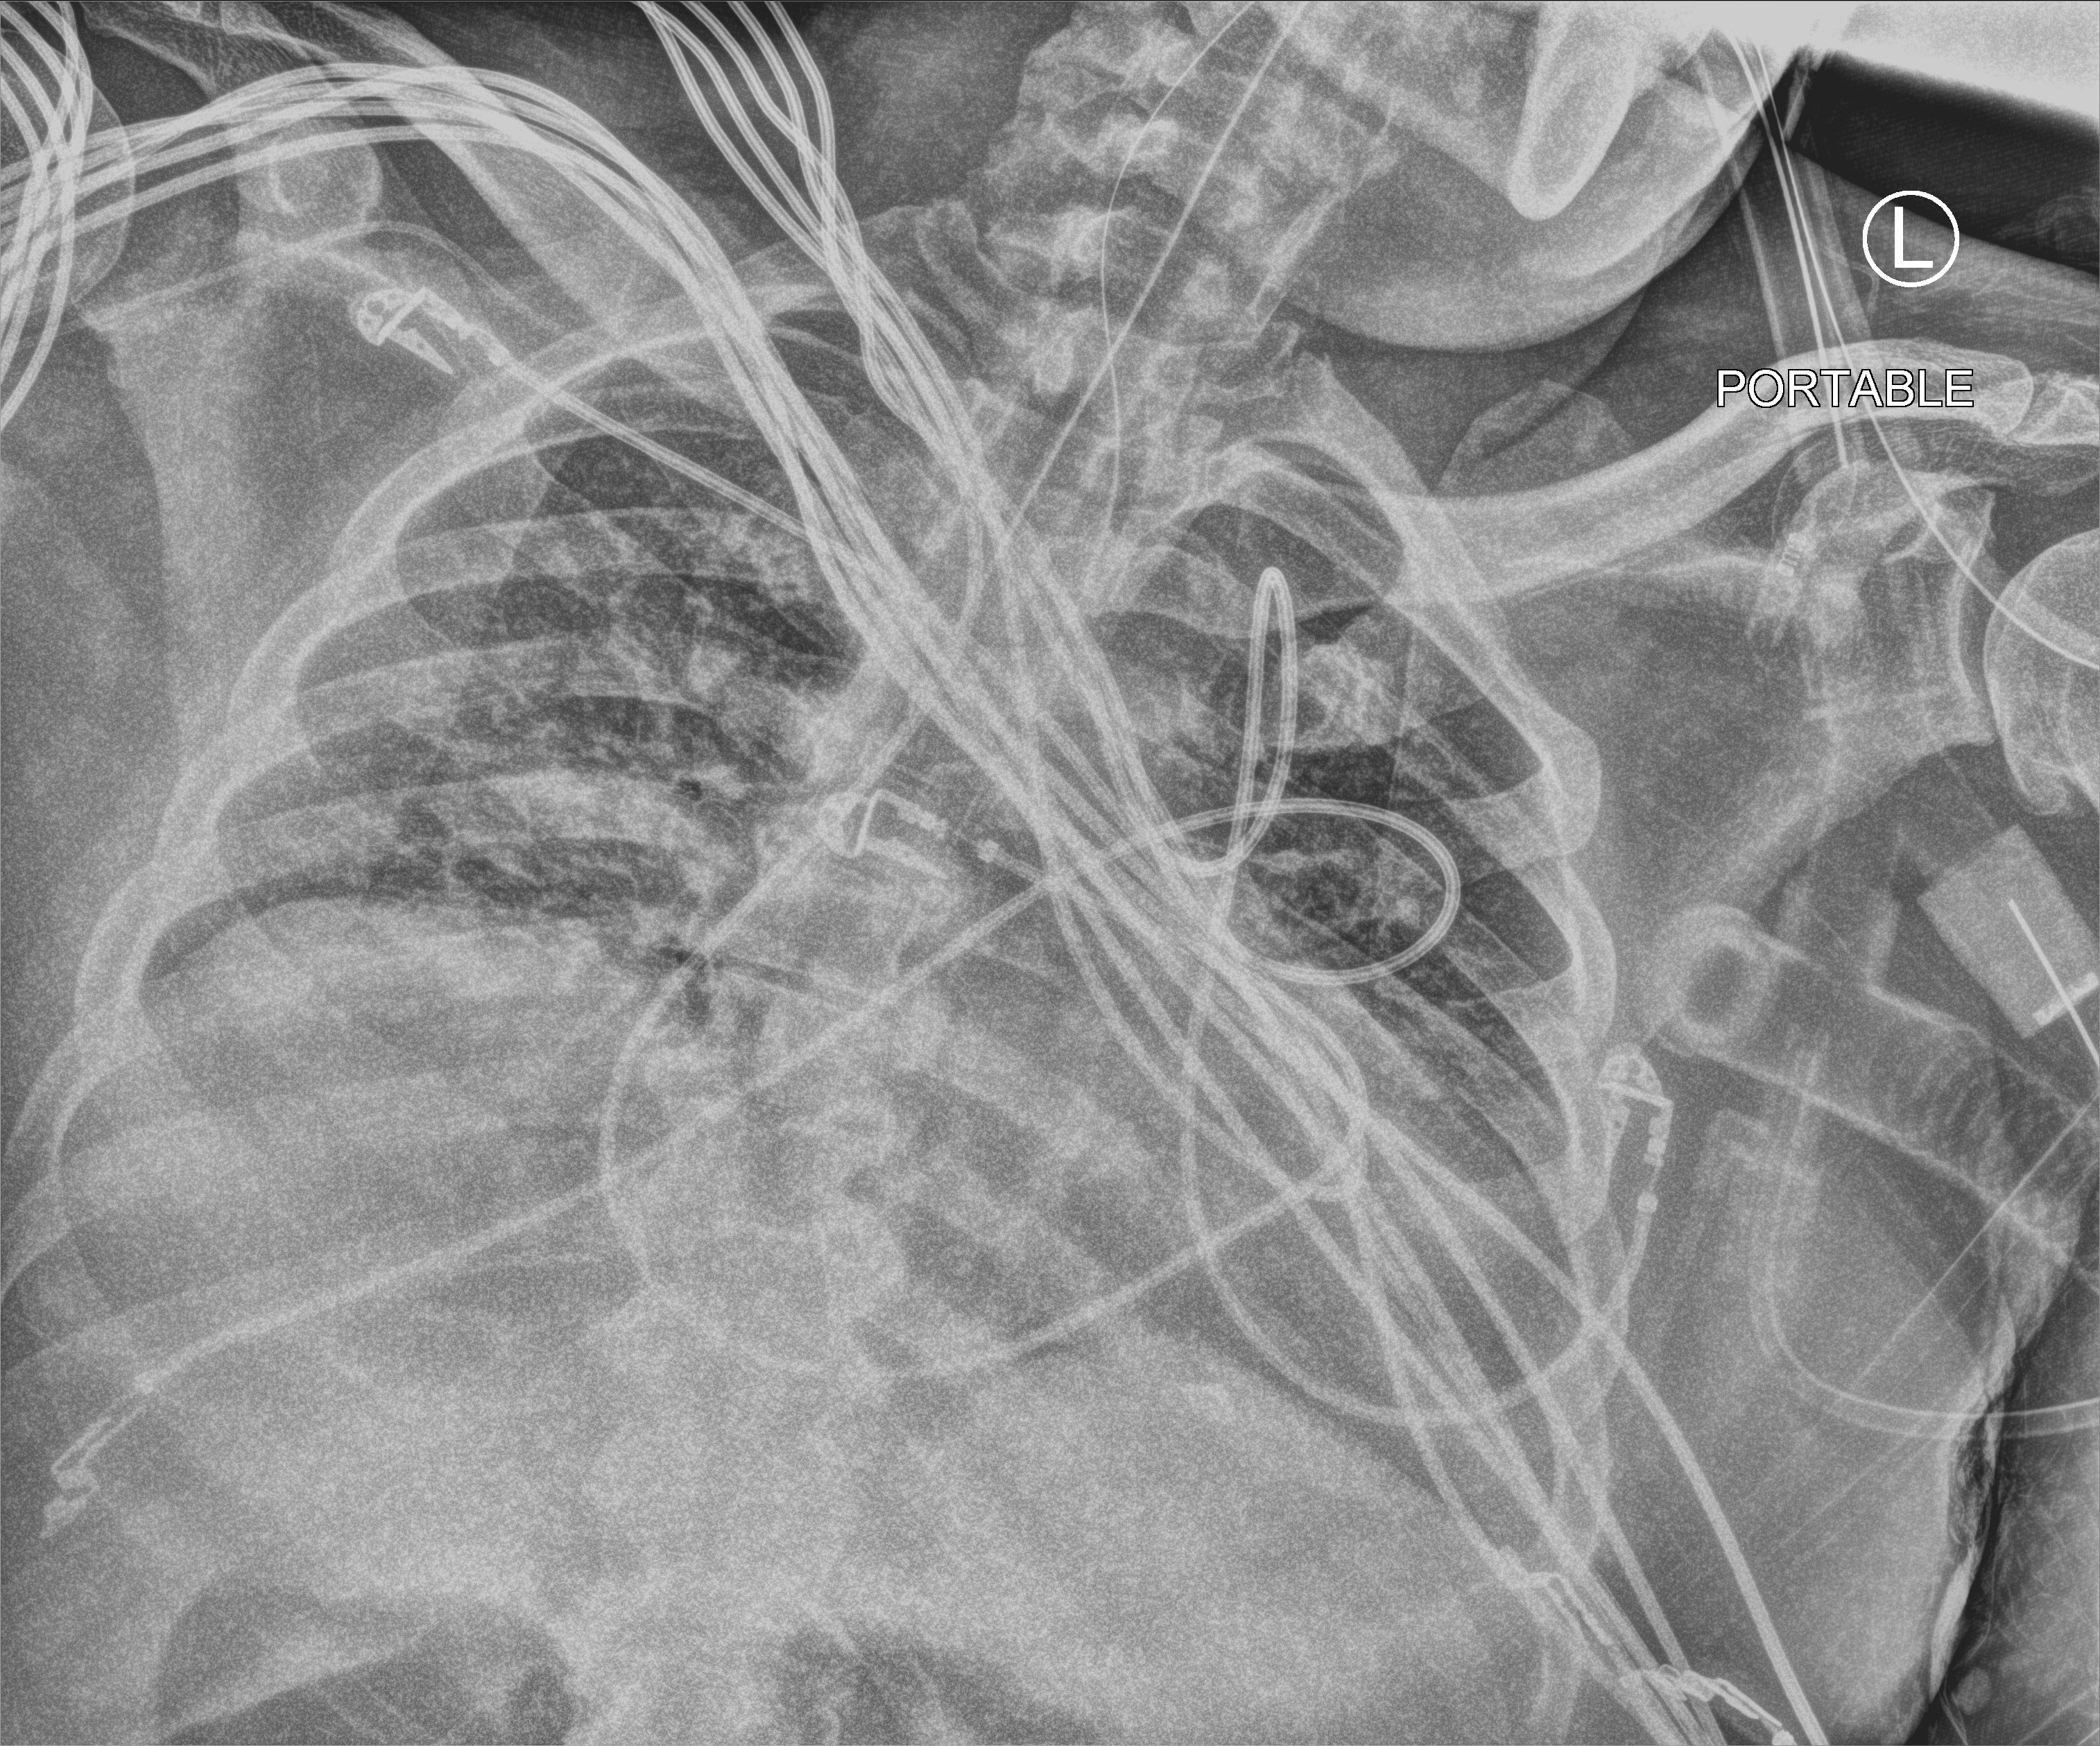
Chest X-ray (portable), anteroposterior (AP) projection. Male patient hospitalised with COVID-19, age 18–59 years.
Admission-level facts for this patient (not findings on this image; timing relative to this image not recorded): other chronic lung disease (admission record): no; admitted to intensive care during this hospital stay: yes.